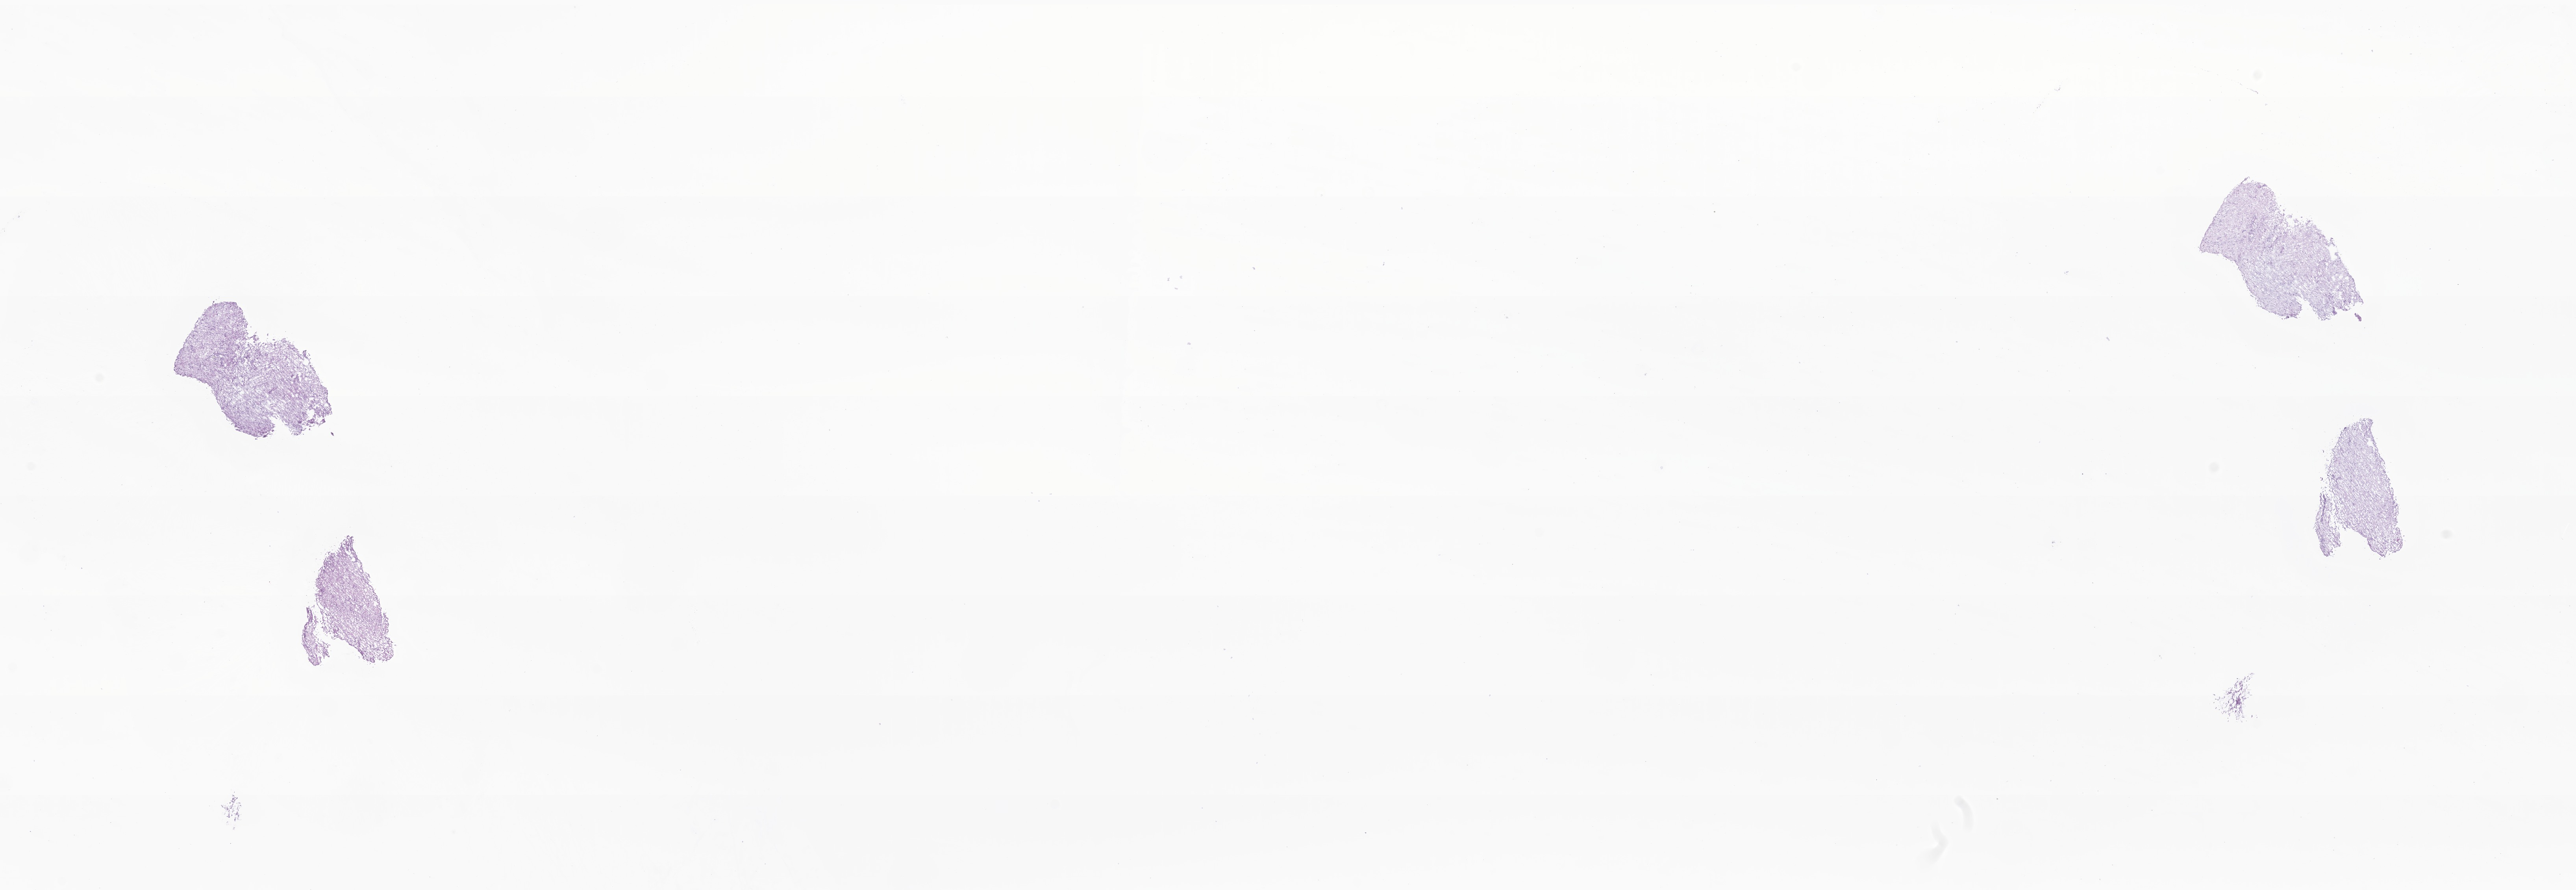
Whole-slide image, haematoxylin and eosin stain of tumor tissue from the temporal lobe, a low-resolution overview of the entire scanned area, about 27.6 x 9.5 mm. Cryosection (OCT / tissue freezing medium). Female patient, age 125 months (10 years 5 months).
Recorded diagnosis: Neoplasm, malignant.